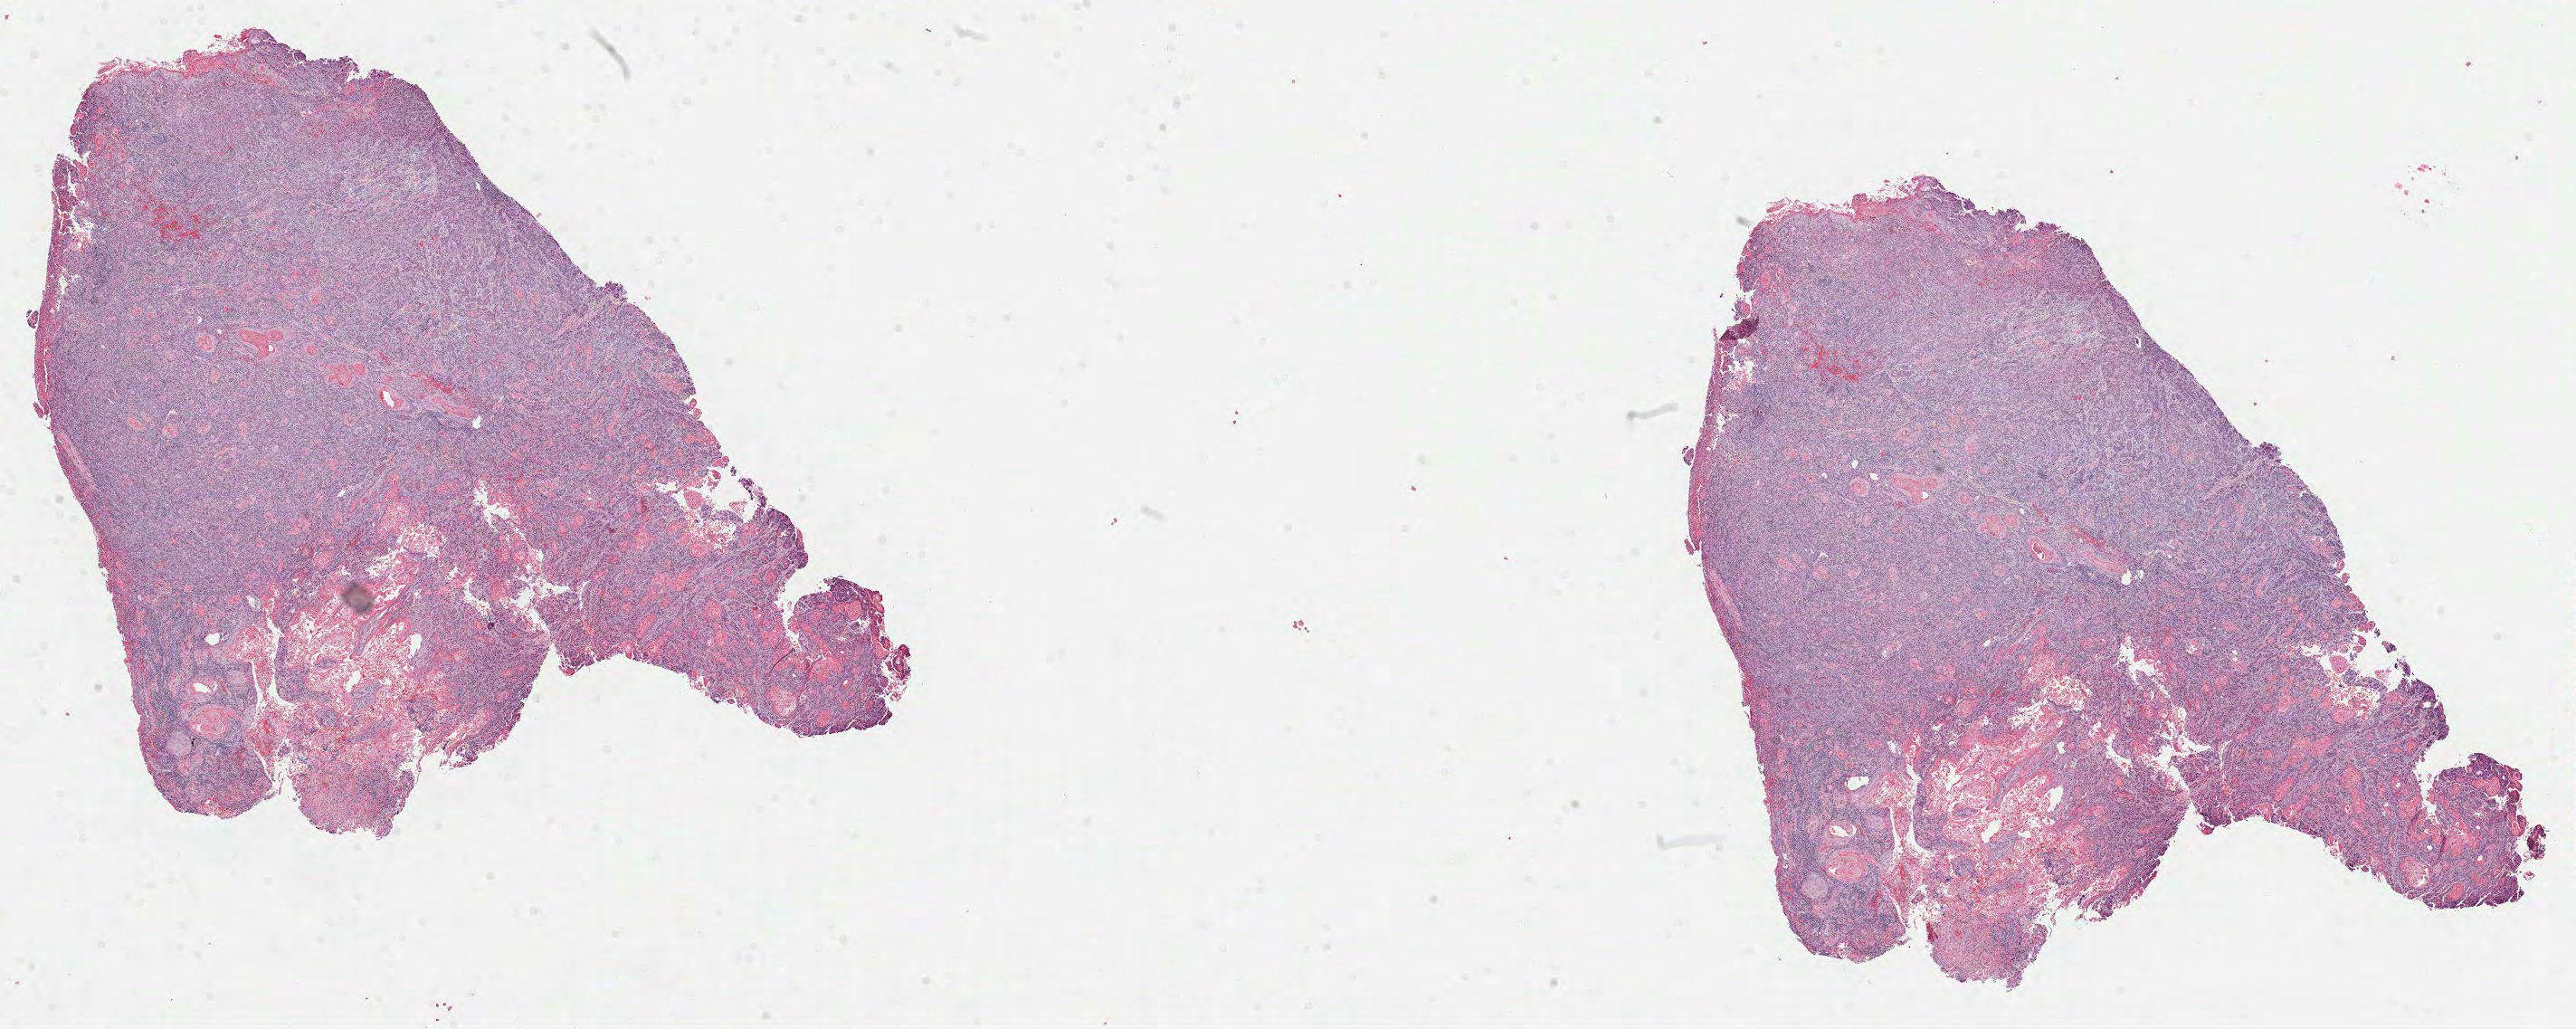
Digitized Hematoxylin and eosin (H&E) stained tissue section (whole slide) — low-resolution overview of the scanned area, about 23.0 x 9.2 mm (slide scanned at 40x); formalin-fixed paraffin-embedded (FFPE) diagnostic section; sample: primary tumour, head and neck. Patient: female, age at initial diagnosis 58 years. Histologic grade: G2 (moderately differentiated).
• TNM: T3 N2b
• AJCC pathologic stage: IVA (7th edition)
• pathologic diagnosis: Squamous cell carcinoma, NOS (tongue, NOS)